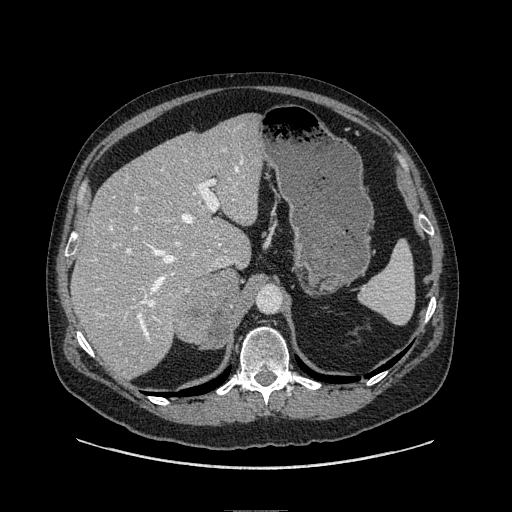
Contrast-enhanced abdominal CT, one axial slice; position 69 of 149 along the scan axis; soft-tissue window (W 400 / L 40 HU); 1.25 mm slice thickness; 512 × 512 image matrix. Male patient. Case-level facts recorded for this patient, not image findings: diagnosis: adrenocortical carcinoma; tumour side: right adrenal; tumour size at pathology: 7.5 cm.
Structures marked on this image (semi-automatically segmented with operator editing):
- mass: bounding box [x1, y1, x2, y2] px = [176, 270, 240, 348]